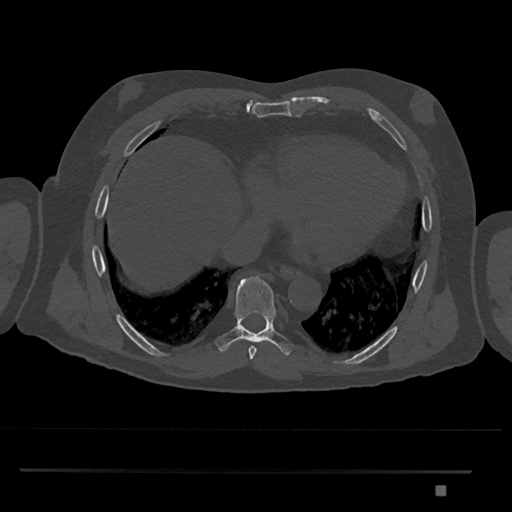
CT including the spine, one axial slice. Slice 1117 of 1134 in the series (ordered by position). Reconstruction kernel Br40s/3. 120 kVp. Bone window (W 1800 / L 400 HU). 0.5 mm slice thickness. 512 × 512 image matrix. Patient: male, 65 years. Case-level facts recorded for this patient, not image findings: primary cancer: prostate.
Structures marked on this image (semi-automatic segmentation, software-assisted and operator-edited):
- T8 vertebra: bounding box [x1, y1, x2, y2] px = [215, 276, 294, 356]